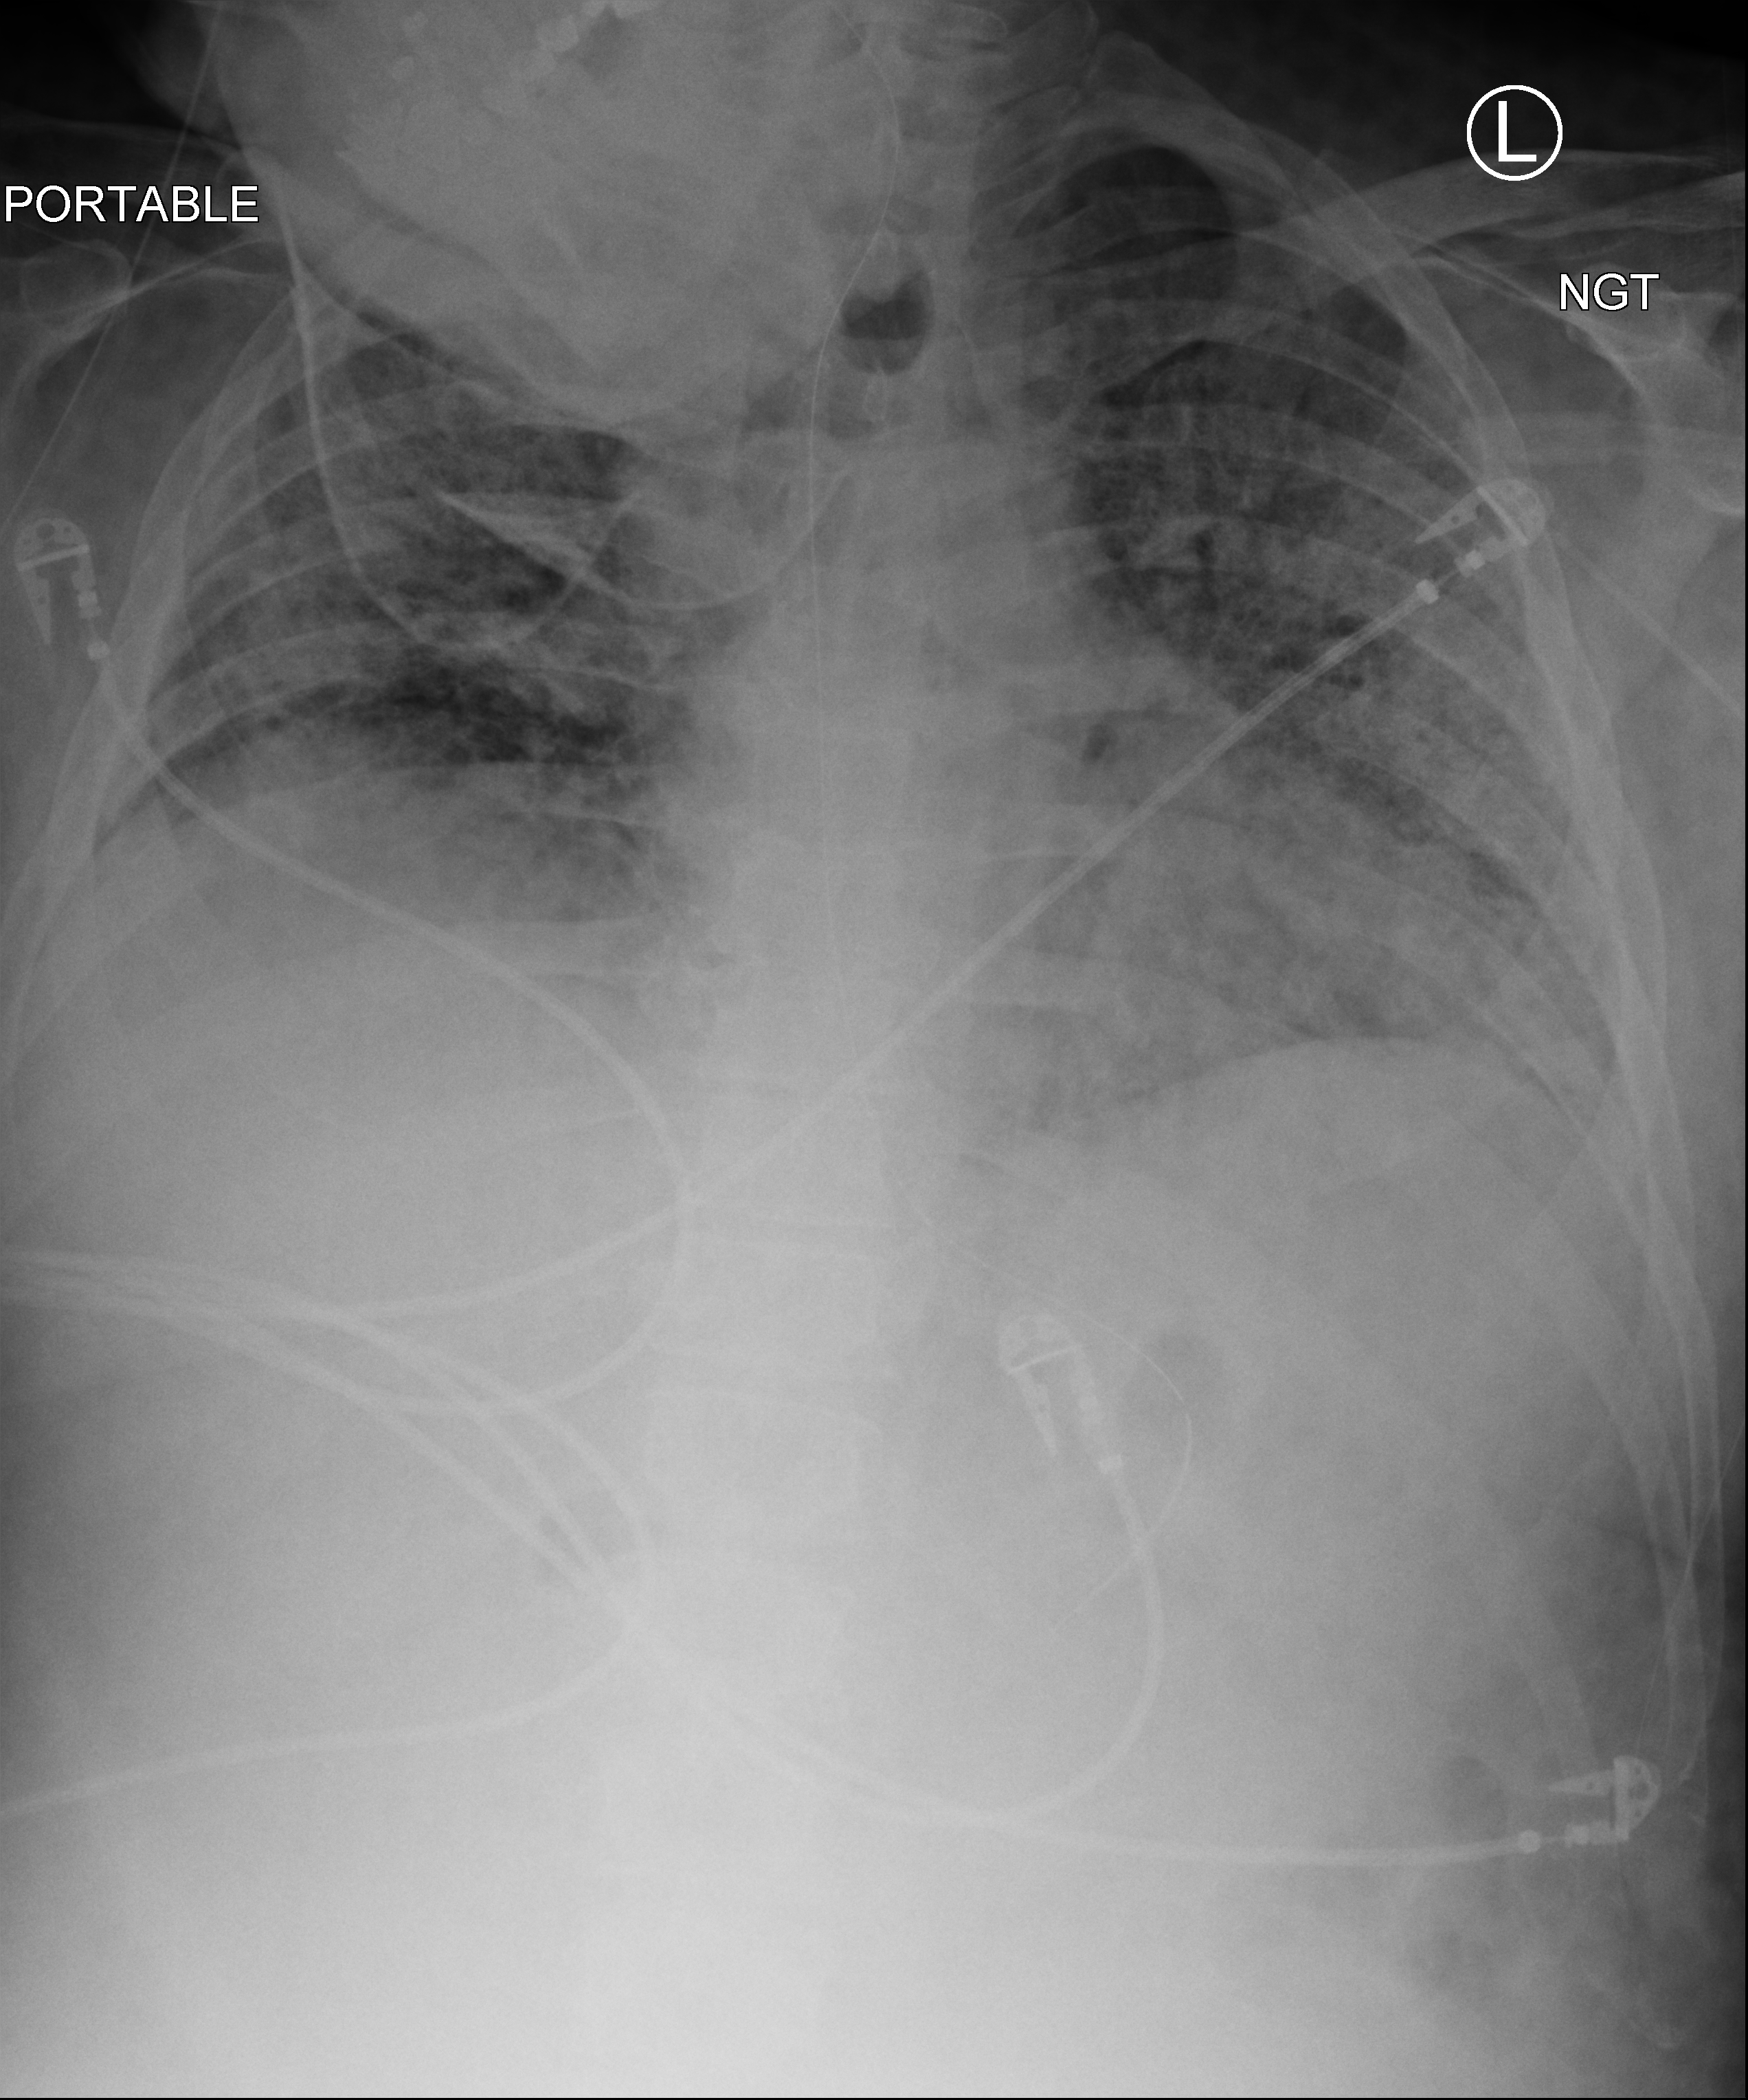
Portable chest radiograph; anteroposterior (AP) projection. Patient hospitalised with COVID-19; male, aged 18–59 years.
Admission-level facts for this patient (not findings on this image; timing relative to this image not recorded): mechanically ventilated during this hospital stay: yes.